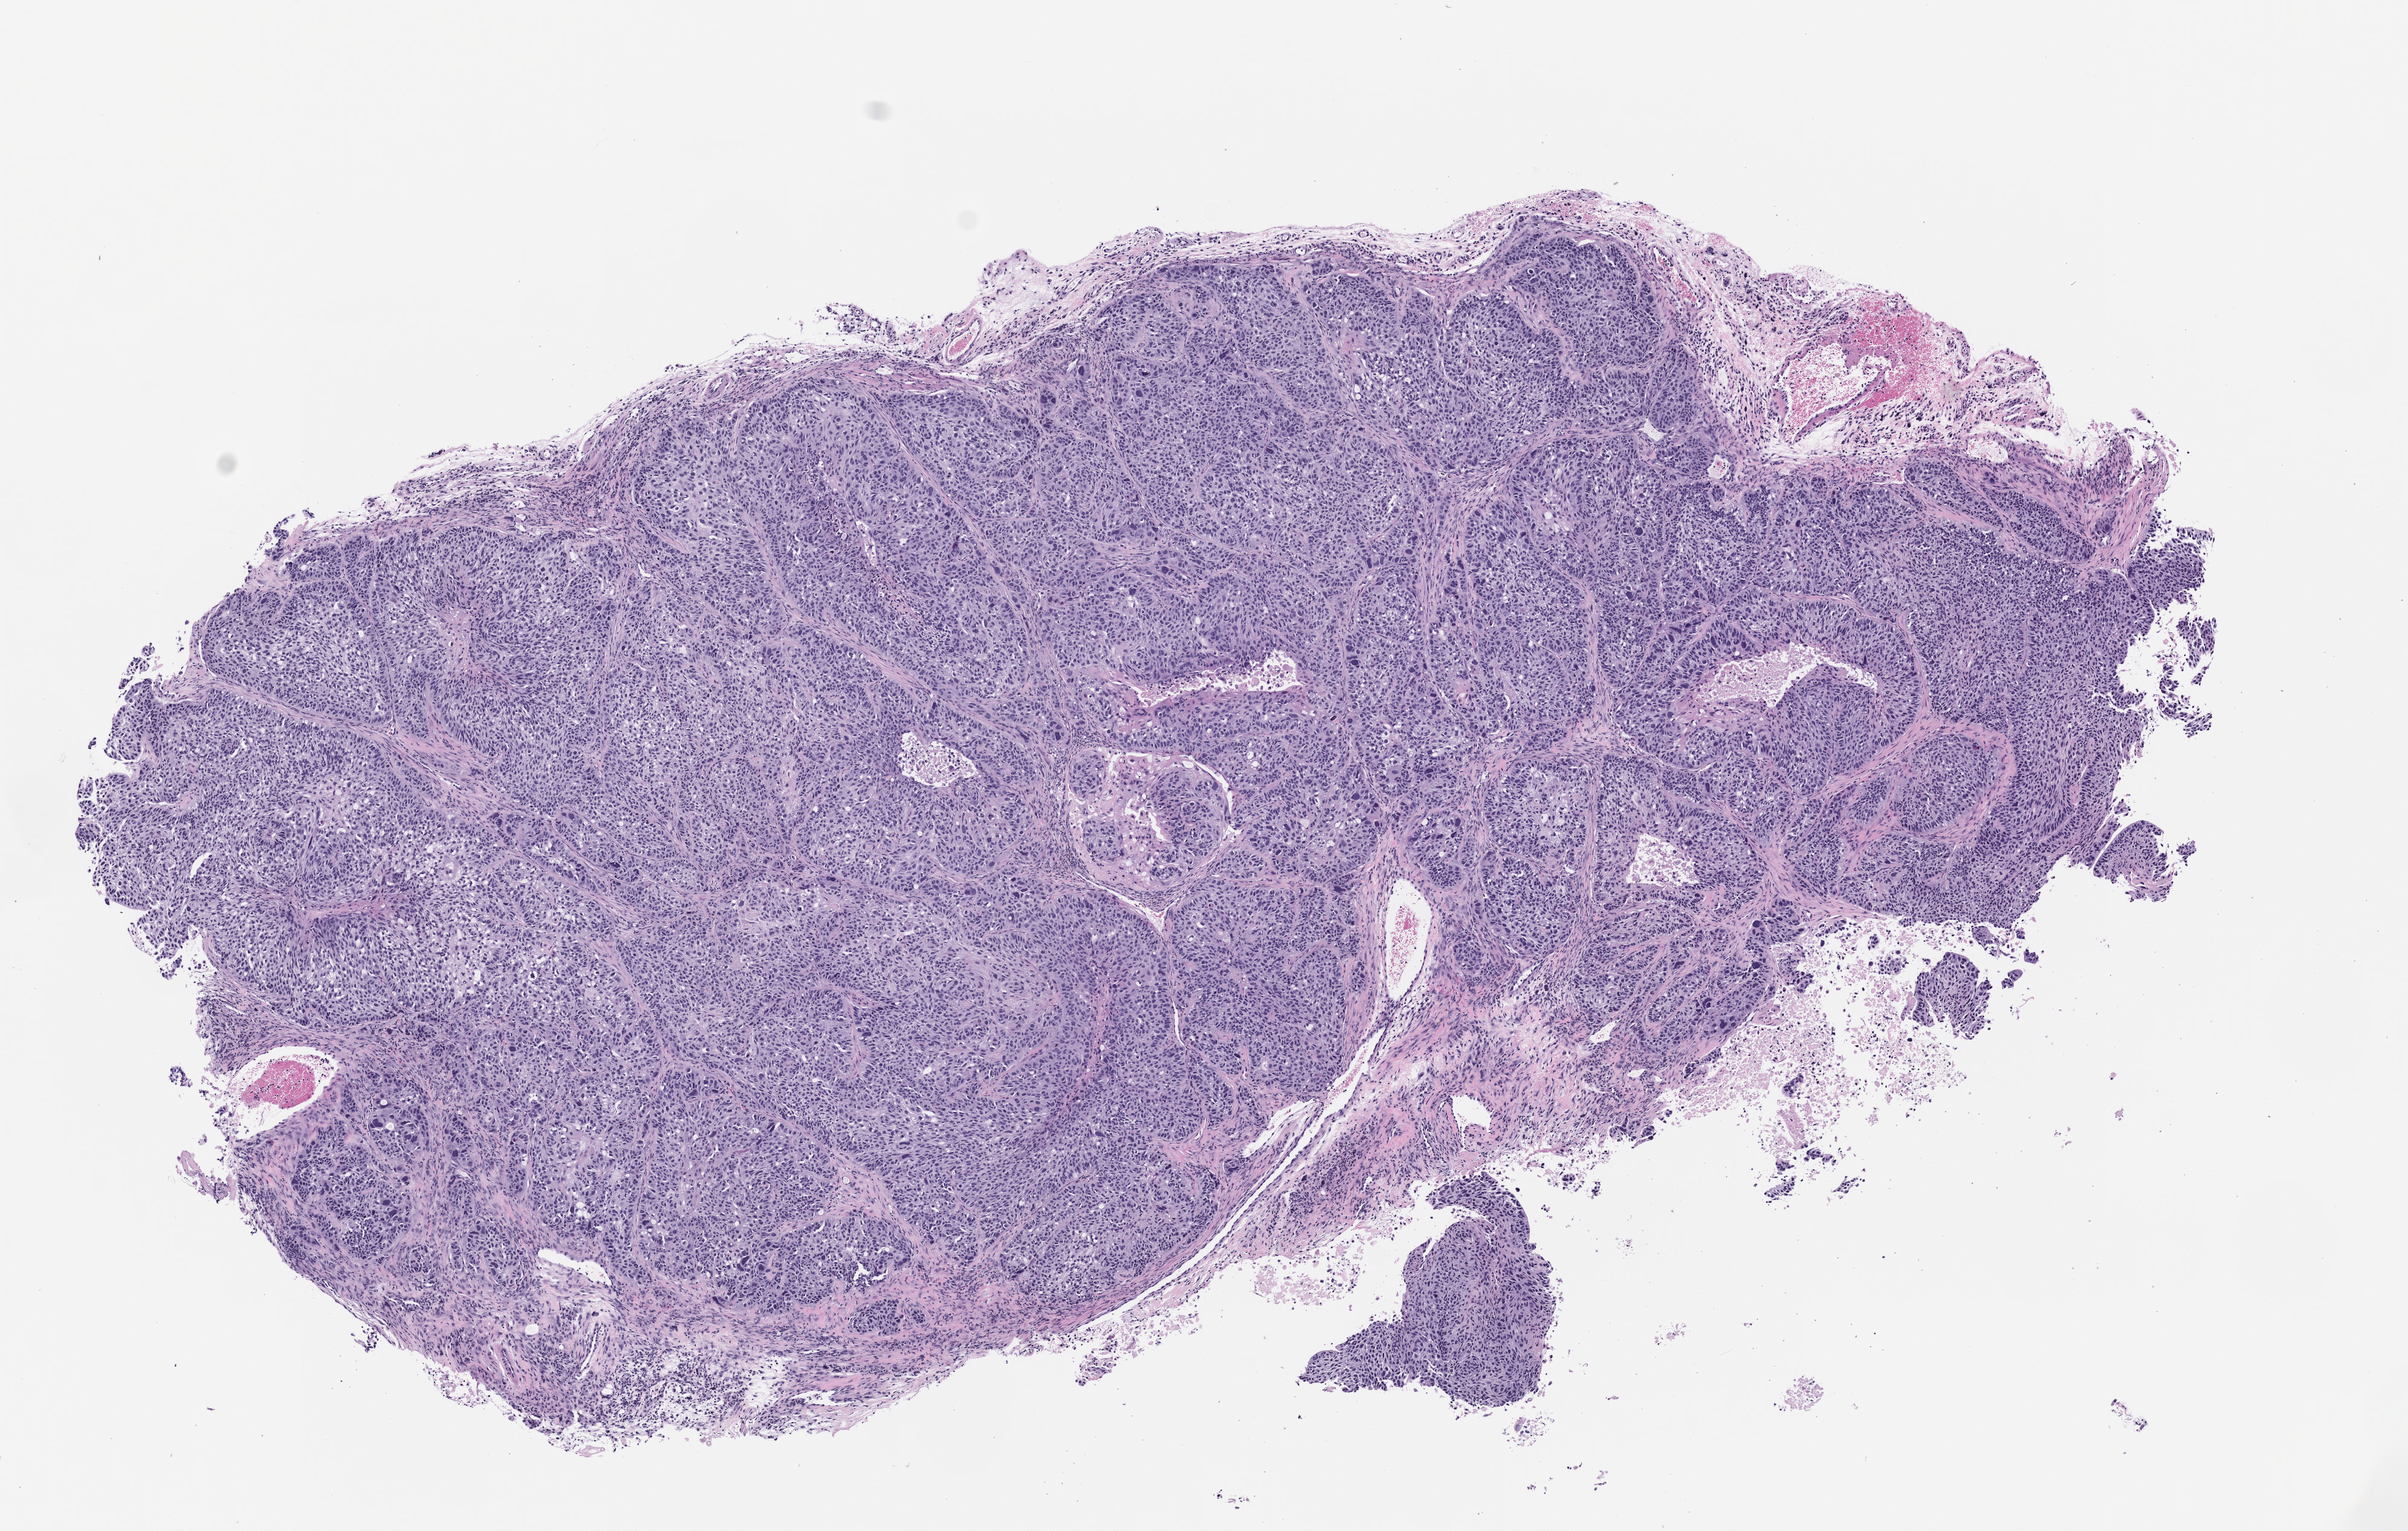
H&E whole-slide image of a patient-derived xenograft (PDX) tumor grown in a mouse, a low-resolution overview of the entire scanned area, about 8.0 x 5.1 mm; formalin-fixed paraffin-embedded section; originating tumor site category: lung.
• originating patient diagnosis: Lung Squamous Cell Carcinoma